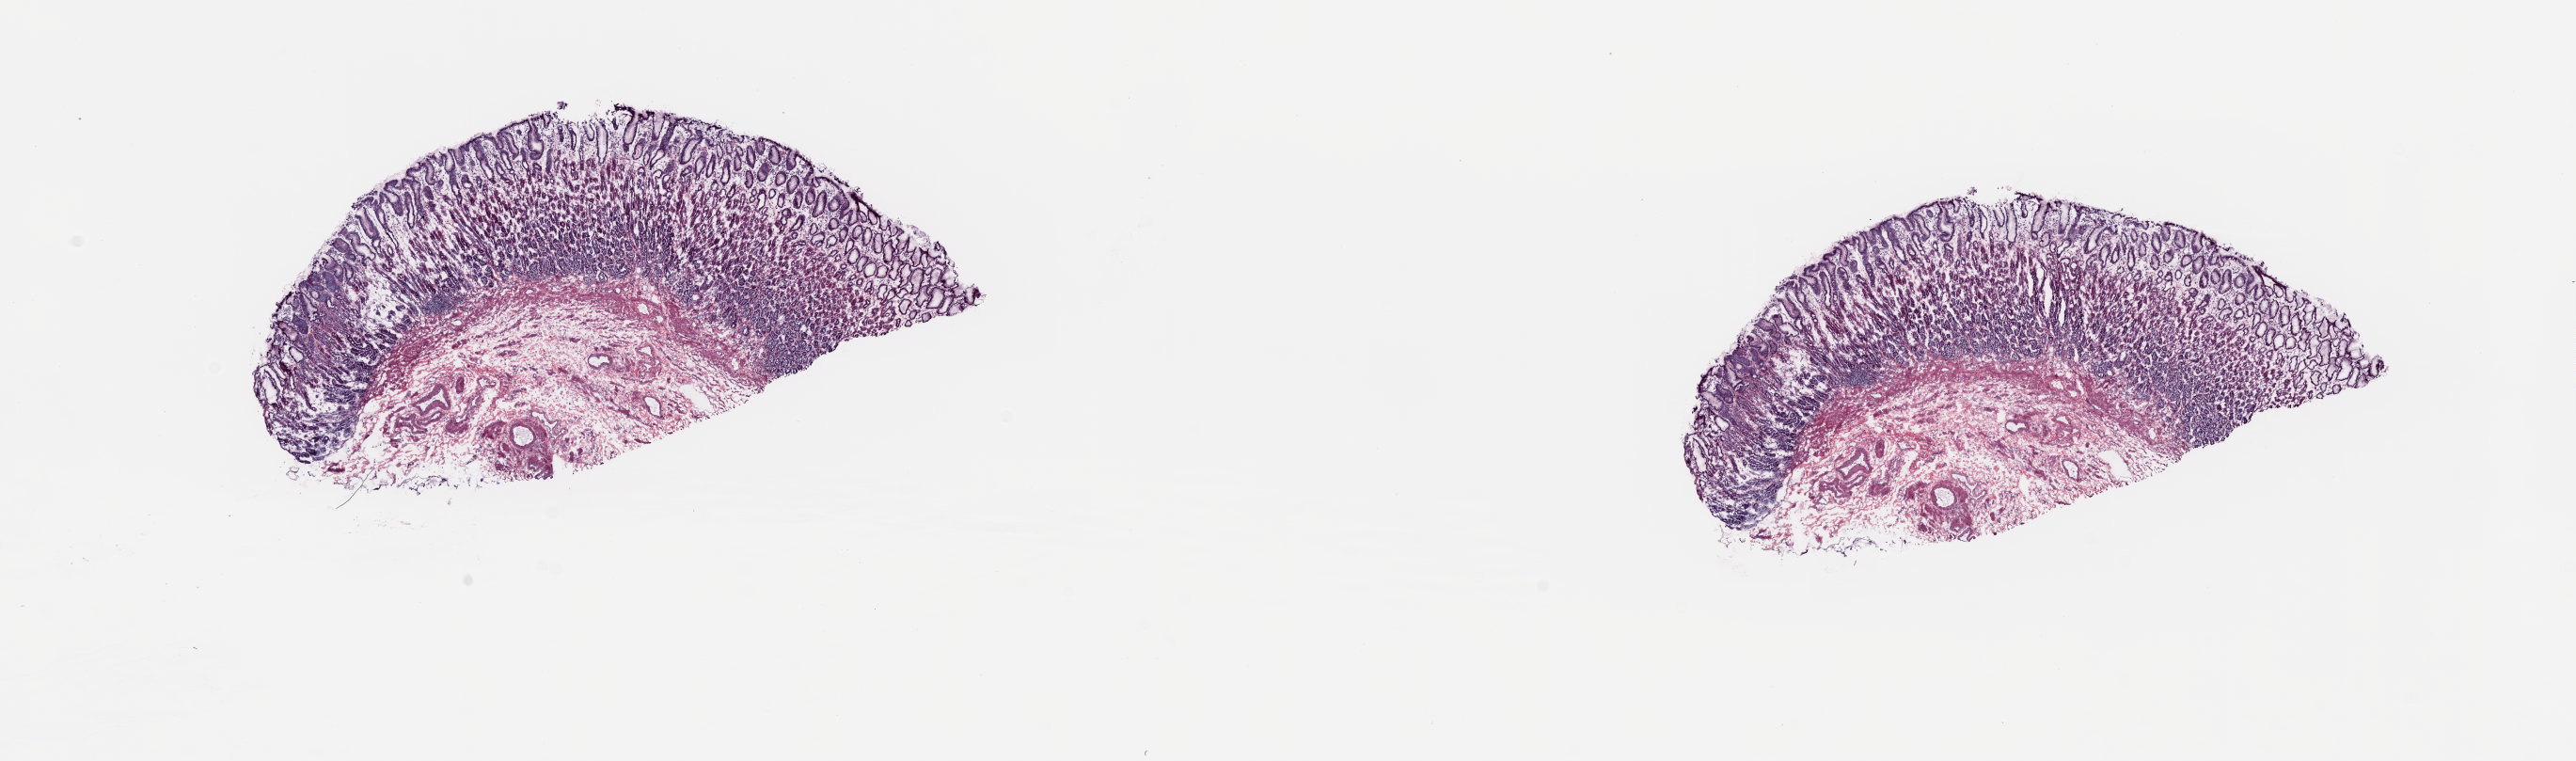
Whole-slide histology image, H&E, low-resolution overview of the scanned area, about 21.6 x 6.4 mm (acquisition: 20x scan), frozen section from the top of the tissue portion, sample: solid tissue normal (non-tumour tissue), esophagus. Male, age 77 years at initial diagnosis. Composition of this section per pathologist review: tumour cells 0%, tumour nuclei 0%, normal cells 100%, stromal cells 0%, necrosis 0%. Inflammatory infiltration, as recorded: lymphocyte infiltration 2%, monocyte infiltration 0%, neutrophil infiltration 0%.
This section: solid tissue normal (non-tumour) sample from the same patient. Patient diagnosis: Adenocarcinoma, NOS (lower third of esophagus).